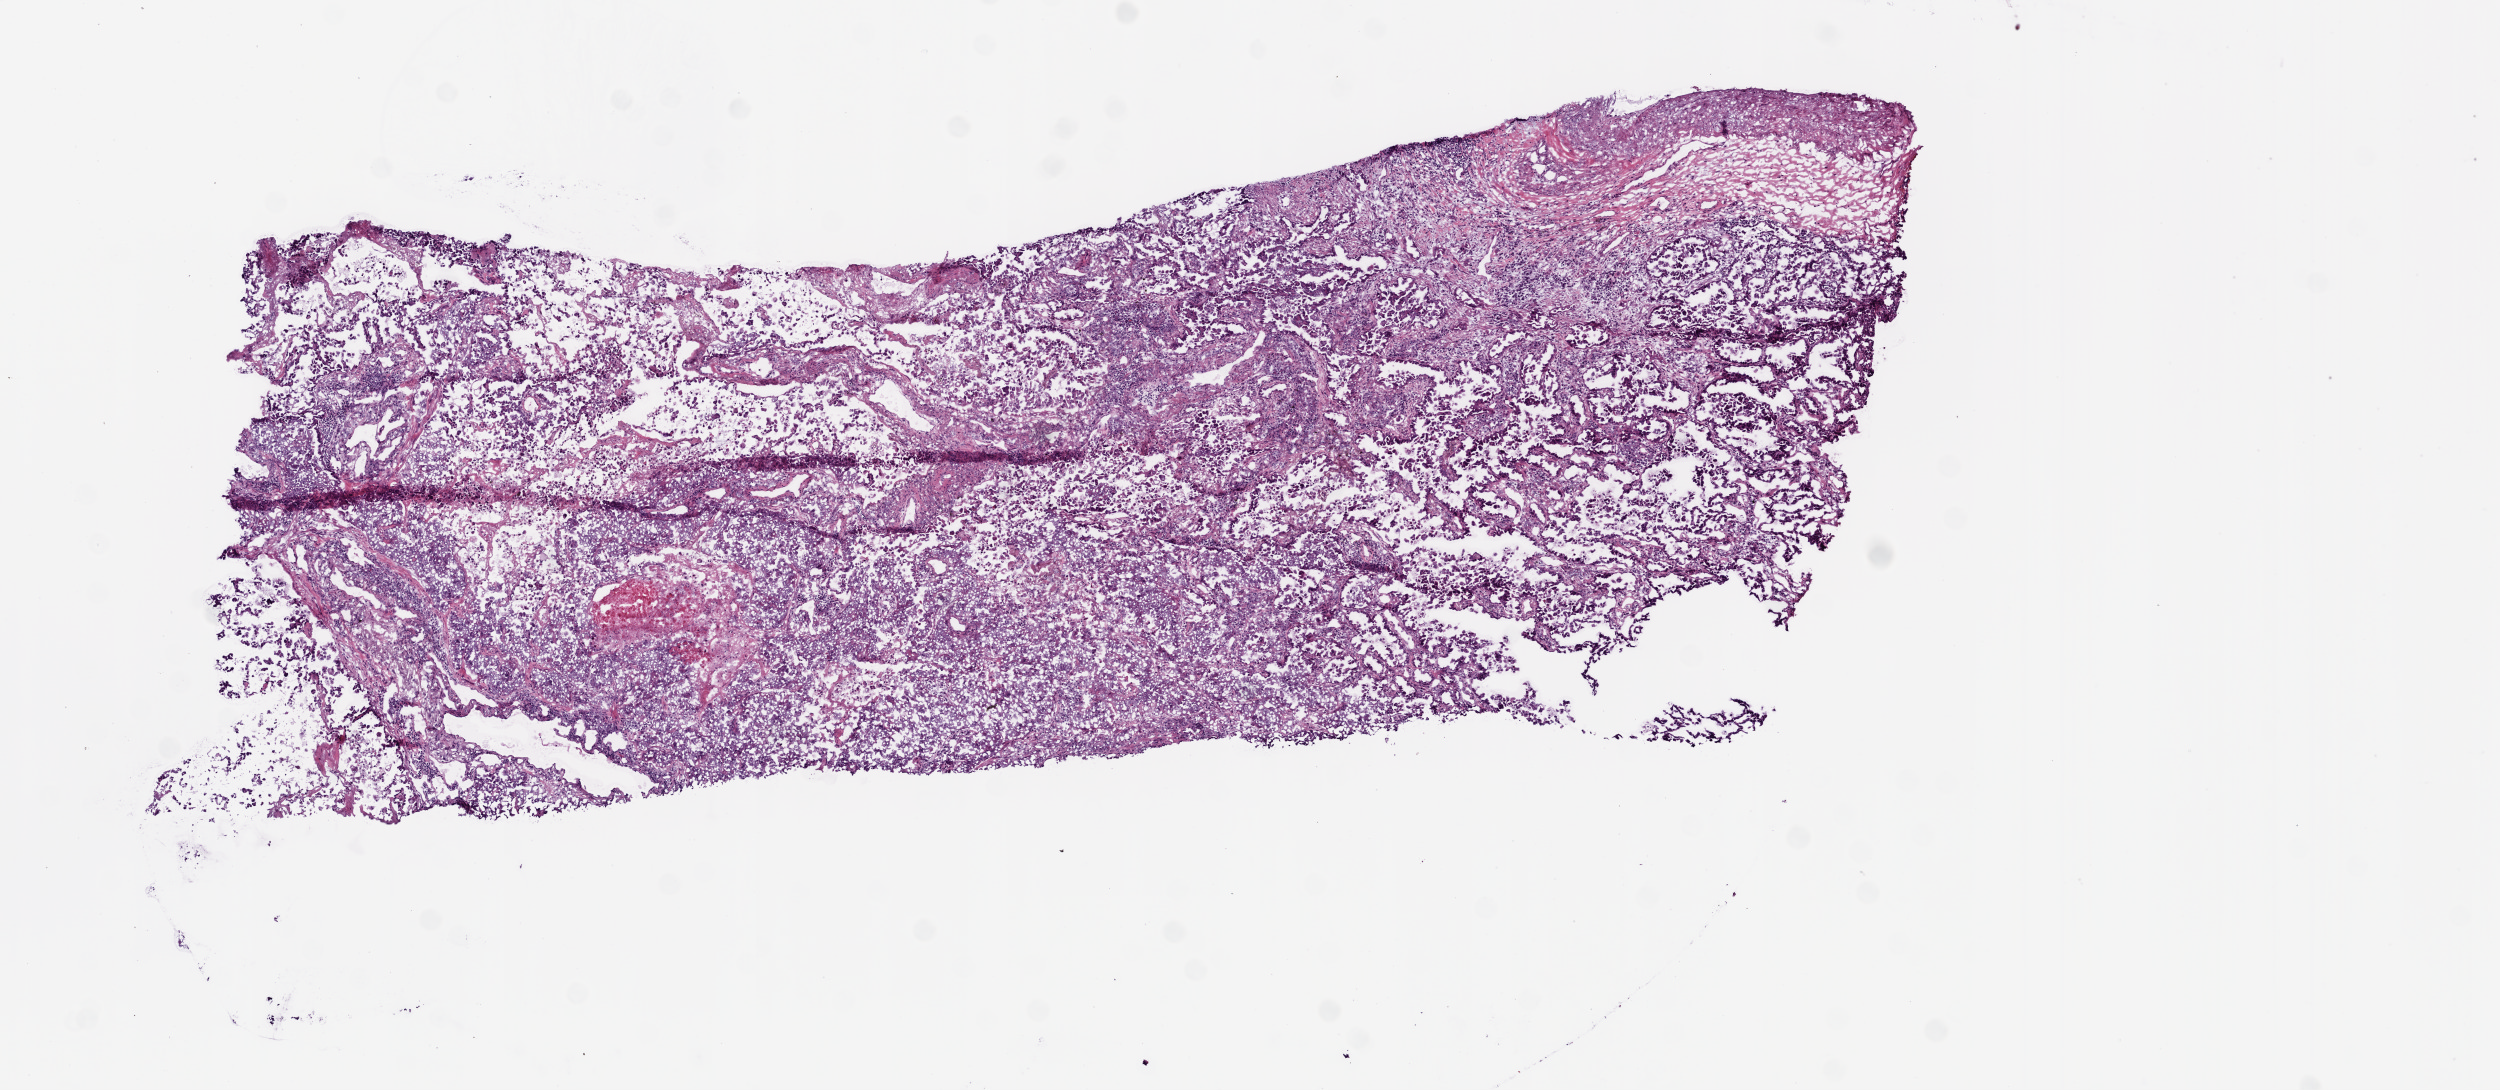
Whole-slide histology image, H&E-stained, low-resolution overview of the scanned area, about 10.0 x 4.4 mm (acquisition: 20x scan). Frozen section from the bottom of the tissue portion. Sample: primary tumour, lung. Female patient; age at initial diagnosis 66 years. Pathologist review of this section (percent, as recorded): tumour cells 95%, tumour nuclei 80%, normal cells 0%, stromal cells 0%, necrosis 5%.
• laterality: left
• AJCC pathologic stage: IIB
• diagnosis: Invasive micropapillary carcinoma (upper lobe, lung)